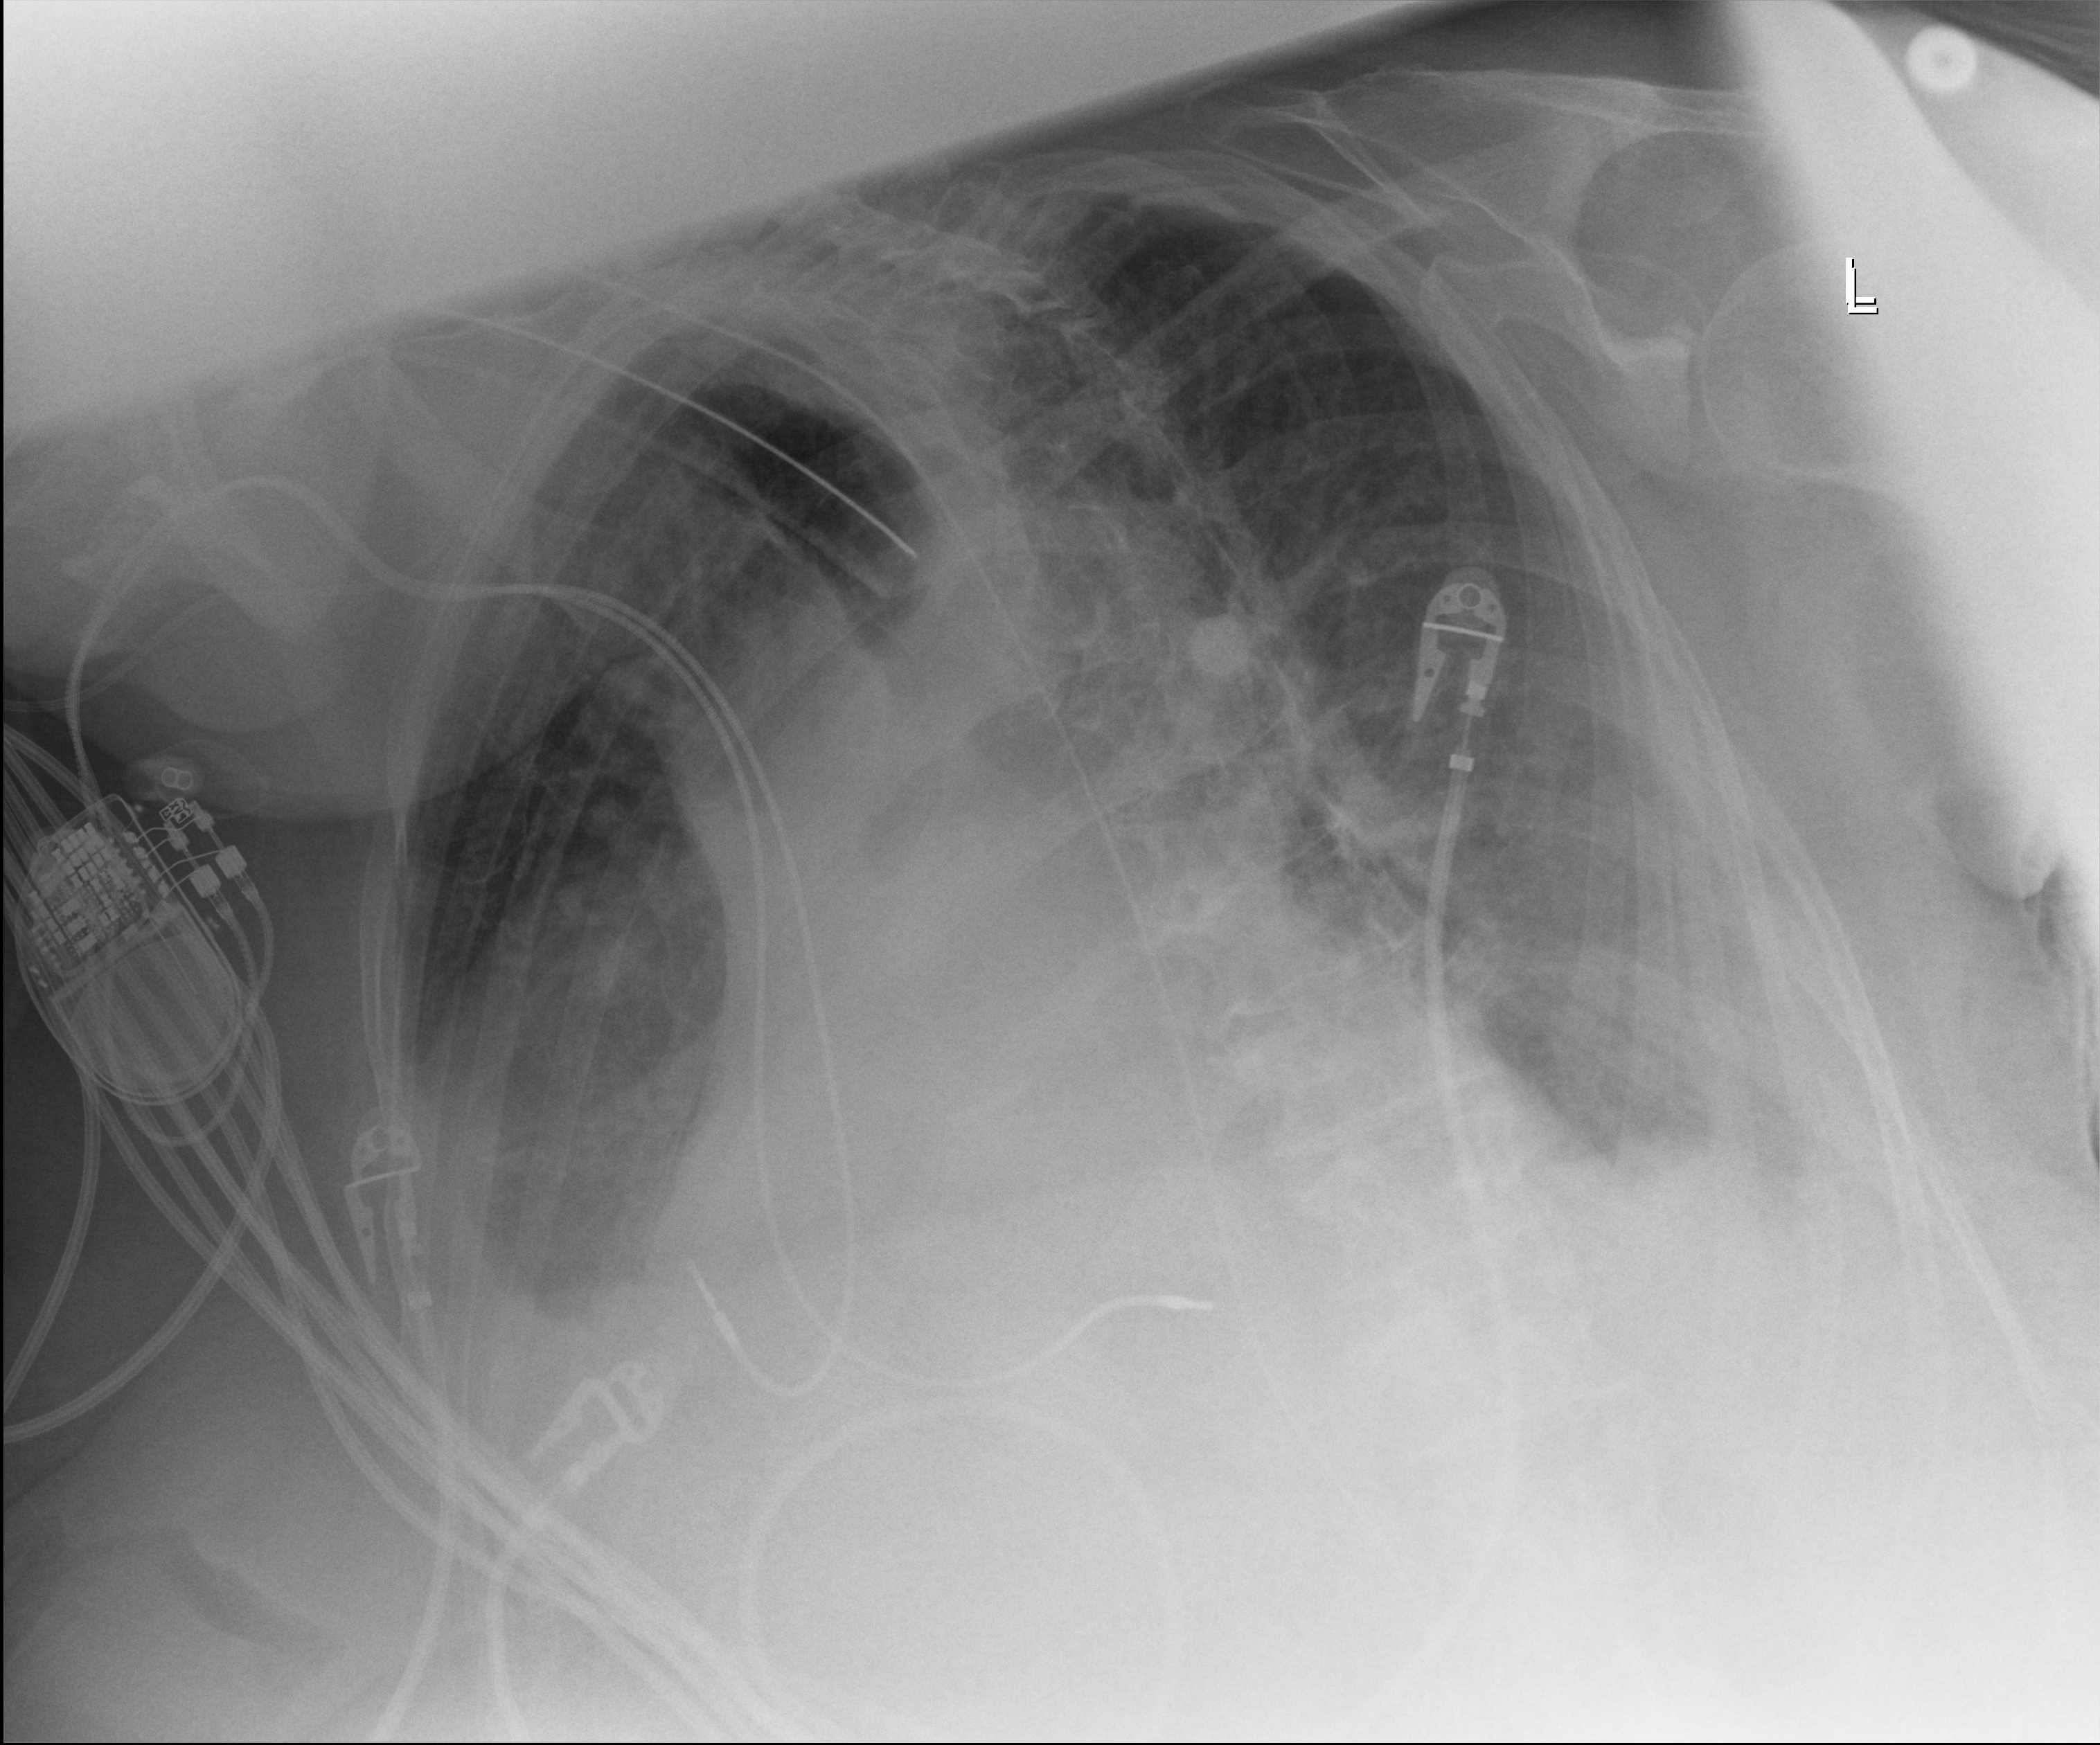
Bedside chest radiograph (digital radiography); anteroposterior (AP) projection. Patient hospitalised with COVID-19; female, aged 75–90 years.
Admission-level facts for this patient (not findings on this image; timing relative to this image not recorded): admitted to intensive care during this hospital stay: yes.